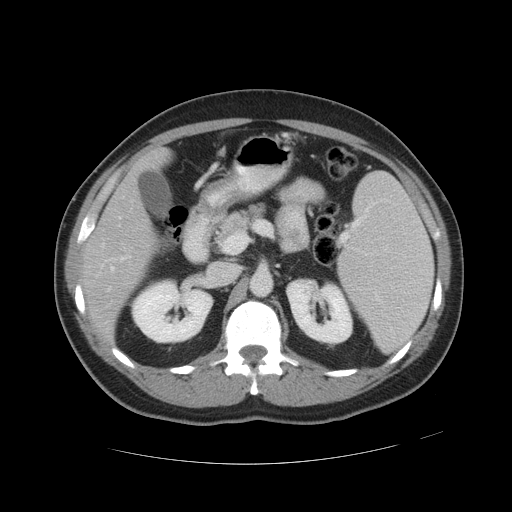
Contrast-enhanced abdominal CT, one axial slice. Position 26 of 49 along the scan axis. Reconstruction kernel STANDARD. Intravenous contrast given. Soft-tissue window (W 400 / L 40 HU). 5 mm slice thickness. 512 × 512 image matrix, field of view 422 × 422 mm. Male patient, age 42 years. From the clinical record (not read from this slice): diagnosis: colorectal cancer liver metastases, imaged before liver resection; multiple liver metastases: yes; largest metastasis: 2.8 cm; disease in both lobes: yes.
Outlined on this slice (outlined manually by an expert reader):
- hepatic veins: bounding box (x1, y1, x2, y2) in pixels: (108, 197, 134, 290)
- liver: (84, 152, 166, 339)
- planned liver remnant (the part of the liver to remain after resection): (84, 234, 153, 339)
- portal vein (with intrahepatic branches): (120, 256, 131, 260)